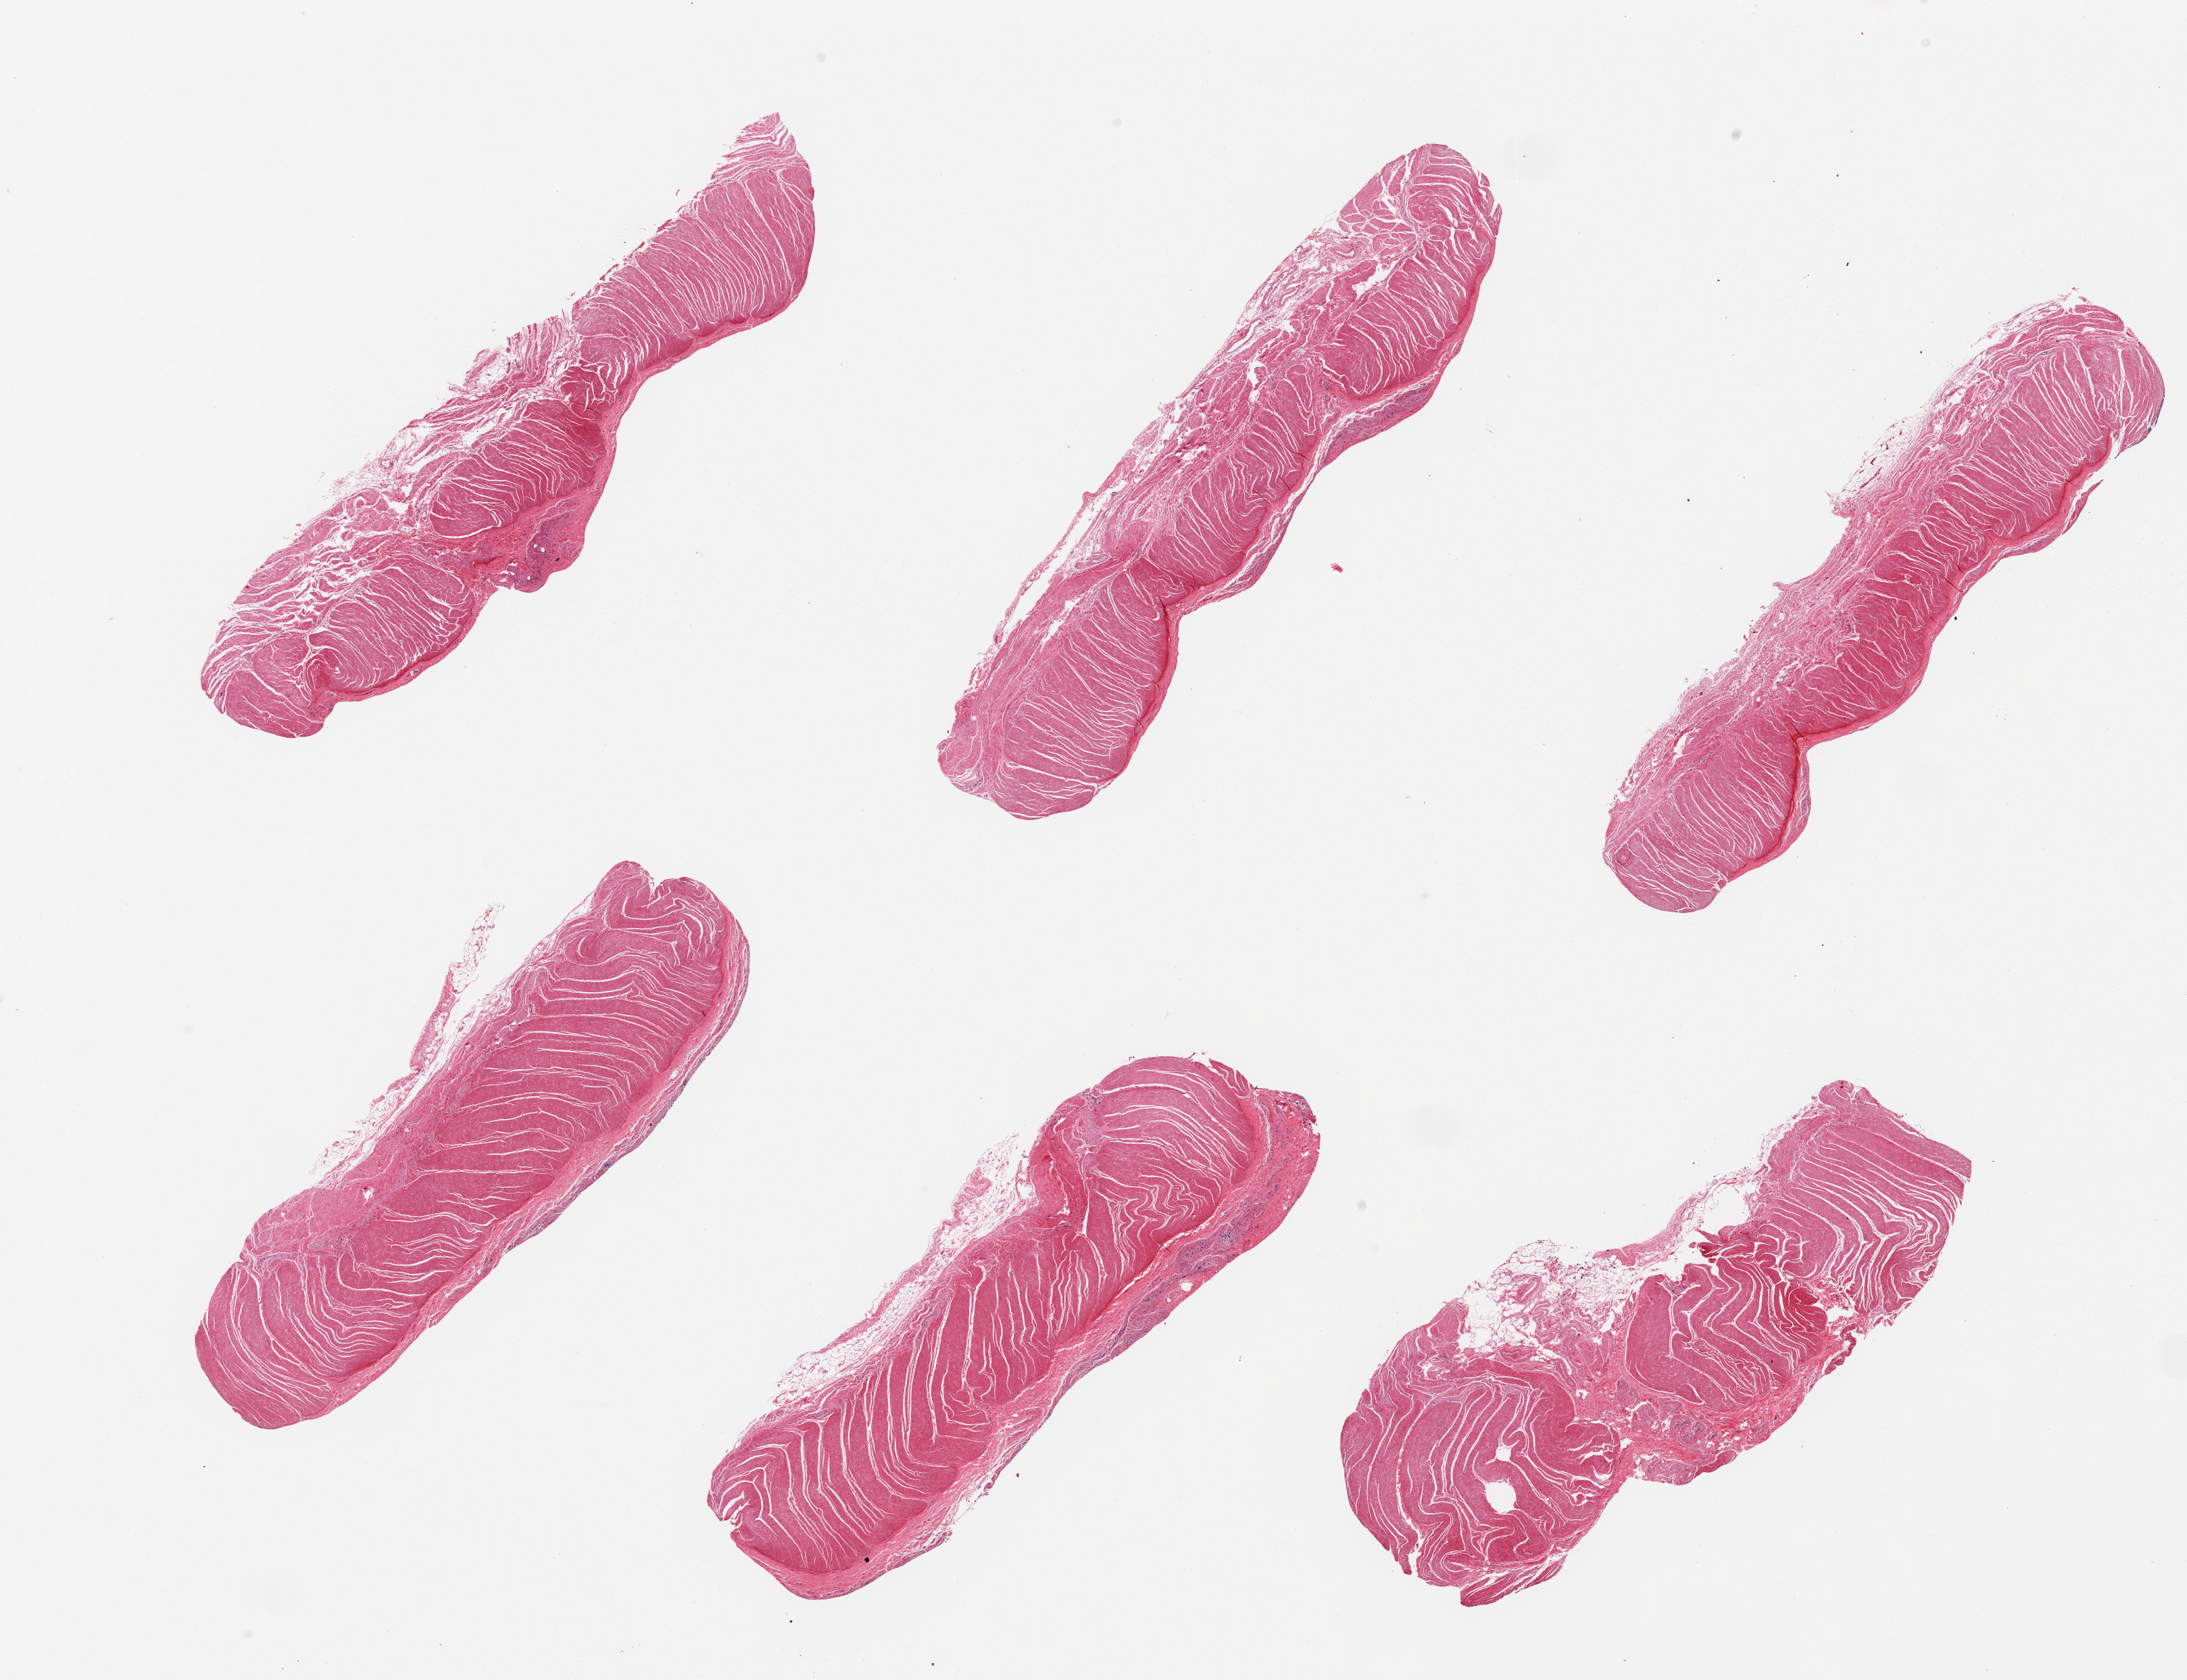
Digitized haematoxylin and eosin-stained section — low-resolution overview of the scanned area, about 25.6 x 19.7 mm, PAXgene-fixed, paraffin-embedded tissue, sampled site (target tissue): sigmoid colon, donor tissue sample.
Reviewer comment on this tissue sample: 6 pieces; well trimmed.